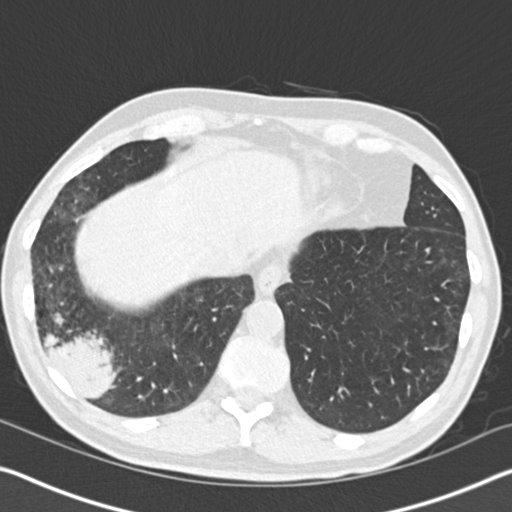
Chest CT (low-dose screening protocol), one axial image, baseline screening round, lung window (W 1500 / L -600 HU), standard (soft-tissue) reconstruction kernel (B30f), 120 kVp, slice 123 of 161 in the series. Male participant, aged 61 years at enrolment.
Lesion marked by an expert reader, bounding box (x1, y1, x2, y2) in pixels: (12, 277, 138, 414). Reader record for this screening exam (exam-level; its link to the box is not recorded): non-calcified nodule or mass ≥4 mm, right lower lobe, 52 × 36 mm, spiculated (stellate) margins, soft tissue attenuation. Official screen result: positive, change unspecified: nodule(s) >= 4 mm or enlarging nodule(s), mass(es), or other non-specific abnormalities suspicious for lung cancer. Participant outcome: lung cancer diagnosed 392 days after this screen (after the second annual screen) — bronchiolo-alveolar adenocarcinoma, NOS, right lower lobe, moderately differentiated (G2), stage IIIB (AJCC 6th edition), 90 mm at pathology.